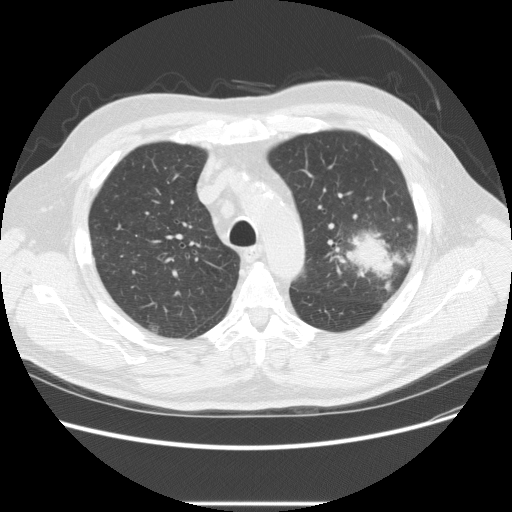
Low-dose screening chest CT, one axial slice. Position 169 of 233 along the scan axis. Reconstruction kernel STANDARD. Lung window (W 1500 / L -600 HU). 512 × 512 image matrix, field of view 380 × 380 mm.
Structures marked on this image (expert manual segmentation):
- lesion 1 (tumor, upper lobe of left lung): bounding box [x1, y1, x2, y2] px = [345, 230, 394, 280]